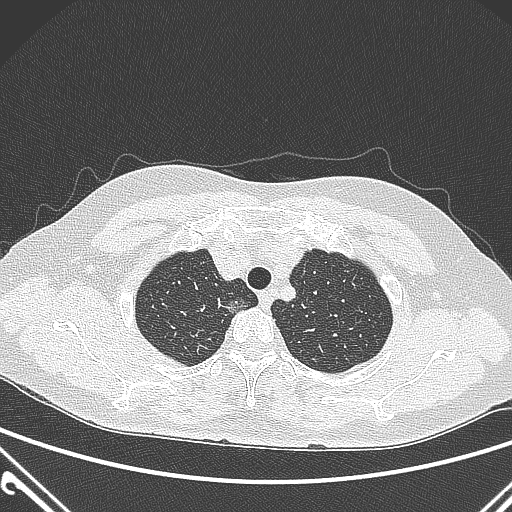
Chest CT, one axial slice. Position 241 of 300 along the scan axis. 120 kVp. Lung window (W 1500 / L -600 HU). 1 mm slice thickness. 512 × 512 image matrix. Patient: female, 54 years. From the clinical record (not read from this slice): clinical TNM (as recorded): T1a N0 M0; histopathological grade: G1.
Structures marked on this image (rectangle marked by the reading radiologist):
- lung tumour (recorded histology: adenocarcinoma): bounding box (x1, y1, x2, y2) in pixels: (222, 289, 250, 324)